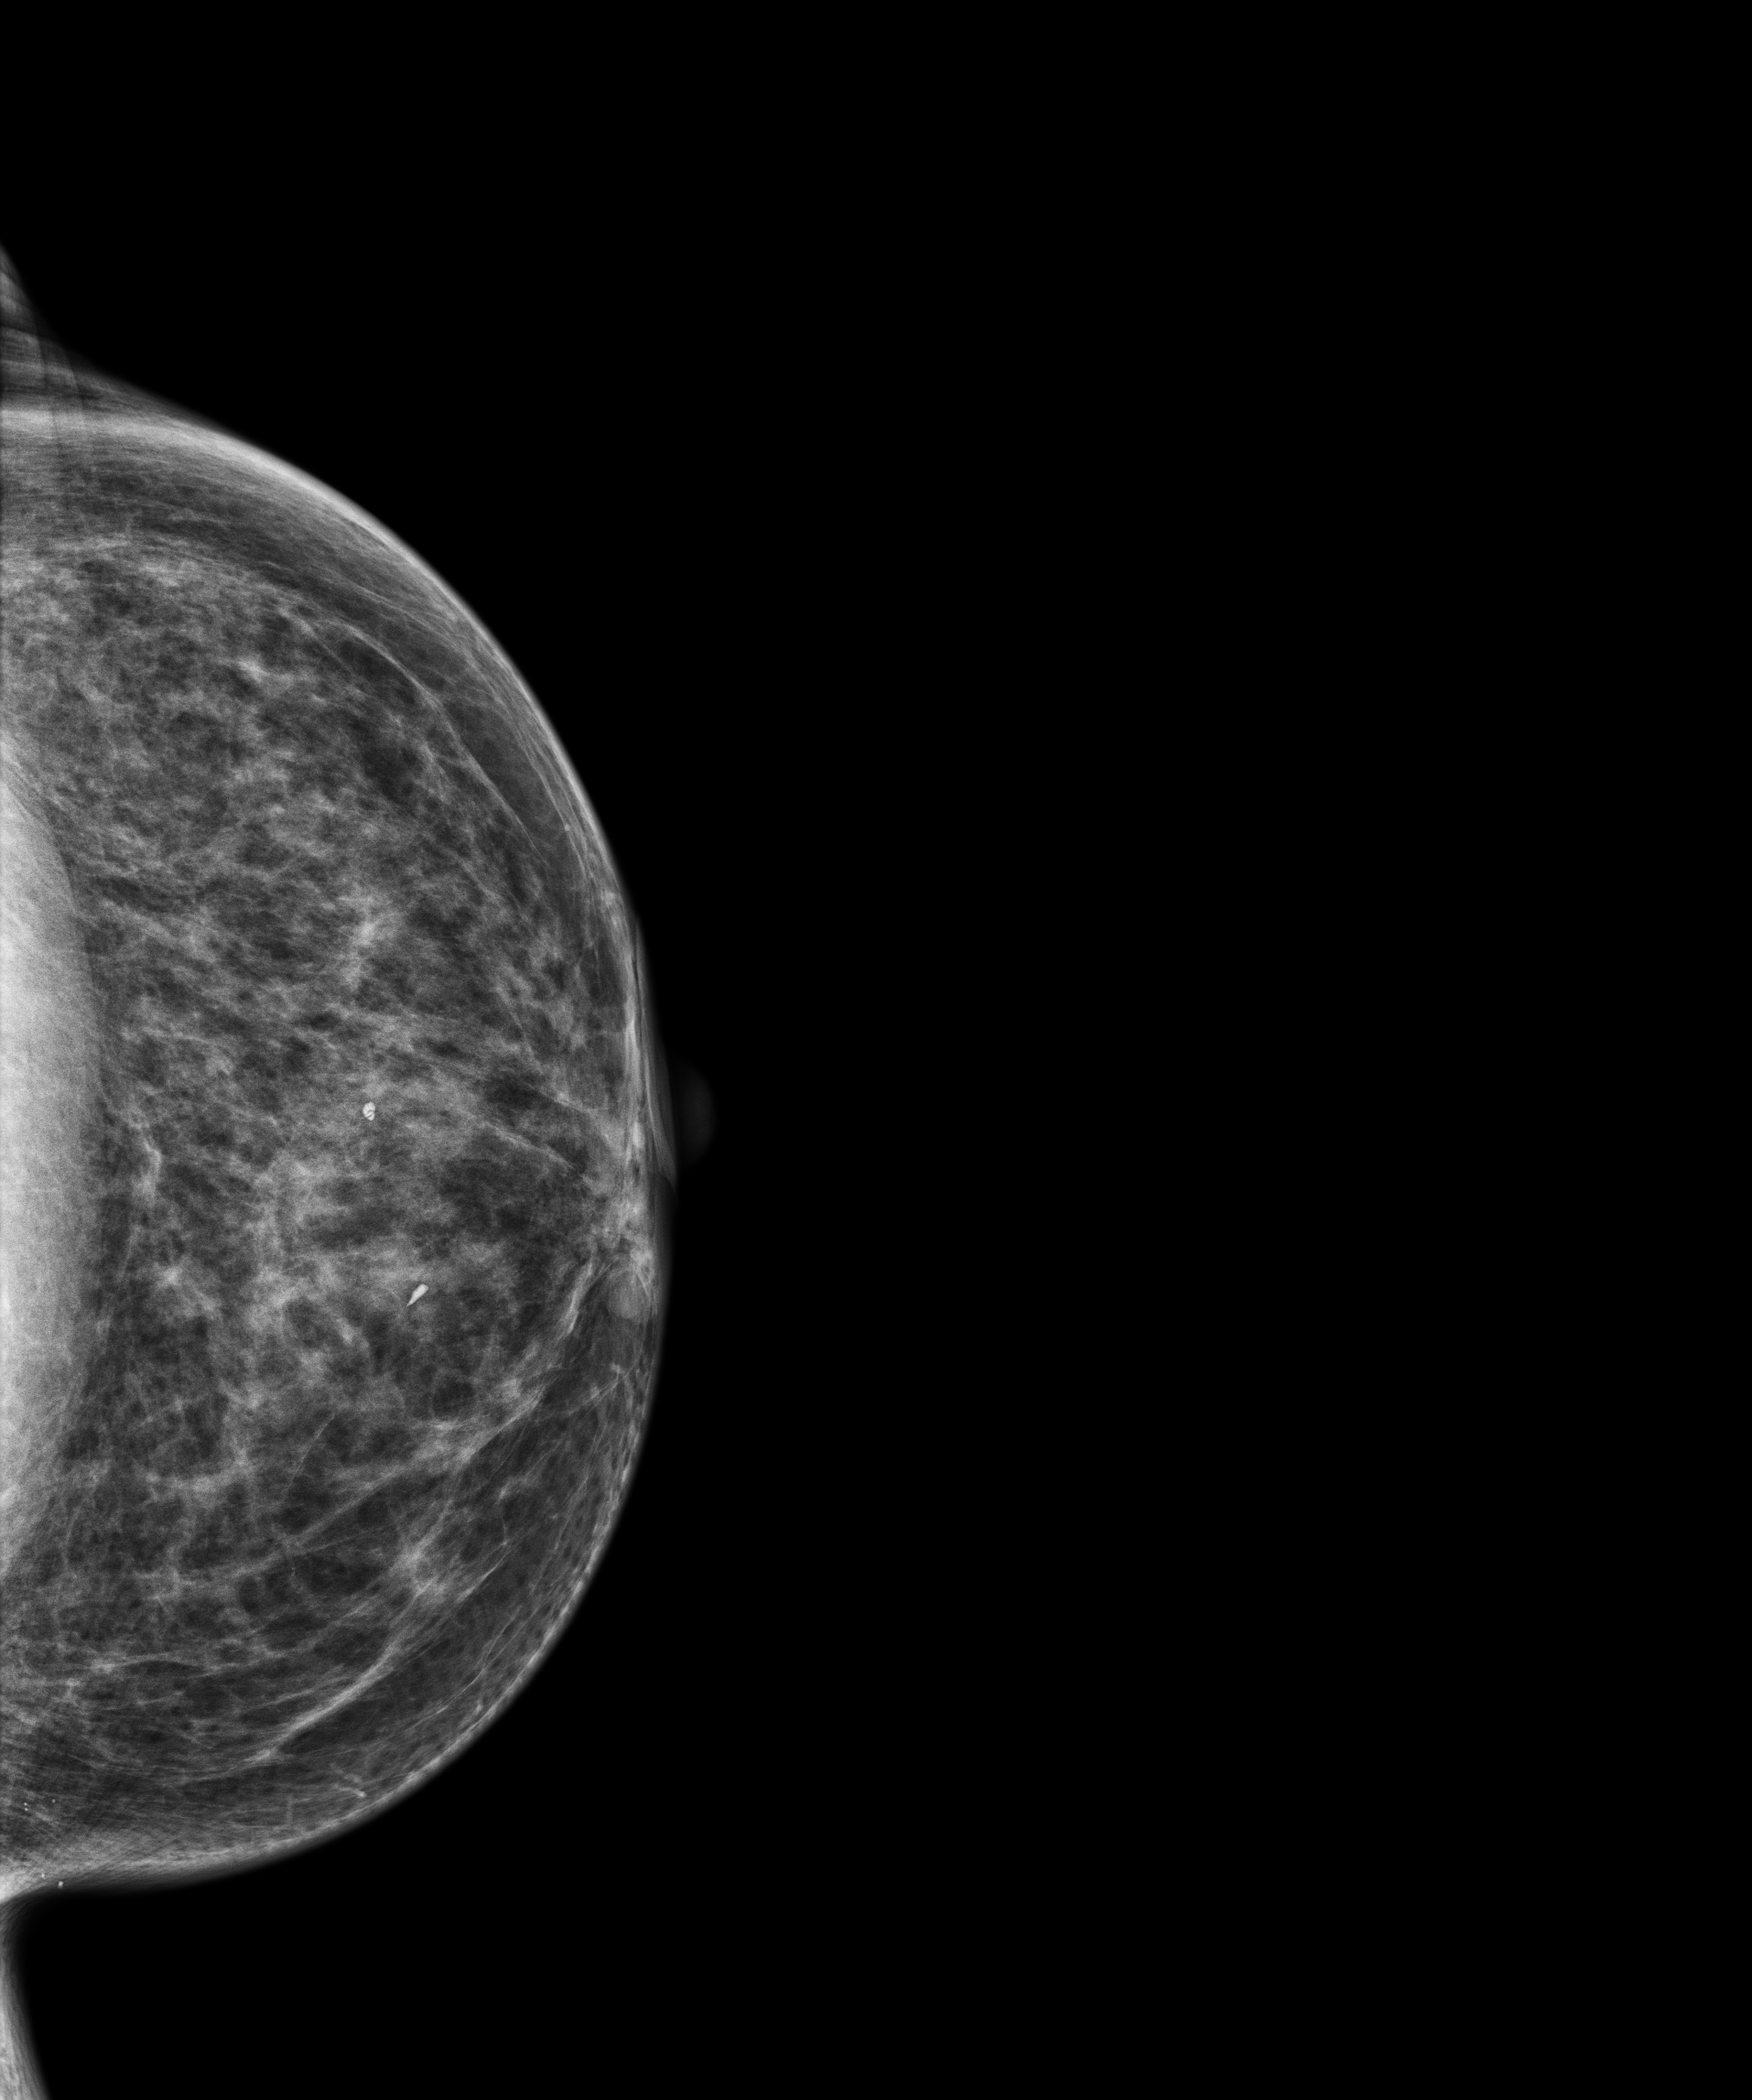
Digital mammogram (FFDM), left breast, CC view, annual screening mammography examination, compressed breast thickness 56 mm. Female patient, age 69 years.
- breast density at the screening exam (both breasts): heterogeneously dense (BI-RADS density category c)
- final BI-RADS assessment for this screening round (tomosynthesis exam, both breasts): category 1
- recall: no recall after this screen